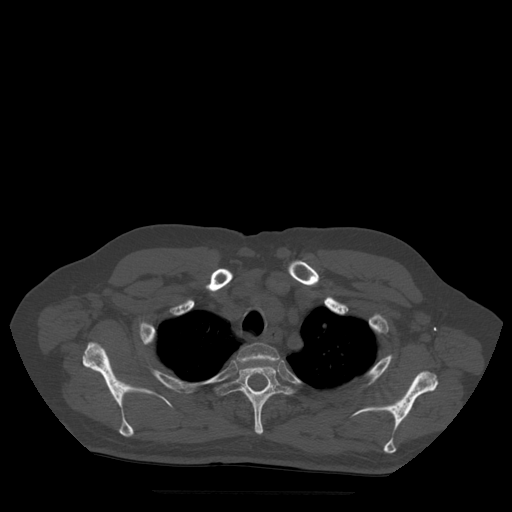
CT including the spine, one axial slice. Slice 412 of 522 in the series (ordered by position). Bone window (W 1800 / L 400 HU). 512 × 512 image matrix. Patient age 72 years. From the clinical record (not read from this slice): primary cancer: prostate.
Annotated regions visible in this slice (semi-automatic segmentation, software-assisted and operator-edited):
- T2 vertebra: bounding box (x1, y1, x2, y2) in pixels: (237, 344, 280, 363)
- T3 vertebra: (216, 364, 293, 435)